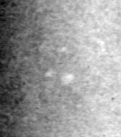
Cropped region of a digitized screen-film mammogram centred on a radiologist-marked abnormality; left breast; MLO view; BI-RADS breast density category 4 (scale 1–4).
Marked abnormality: calcifications, morphology pleomorphic, distribution clustered; BI-RADS assessment category 4; pathology (as recorded): benign.